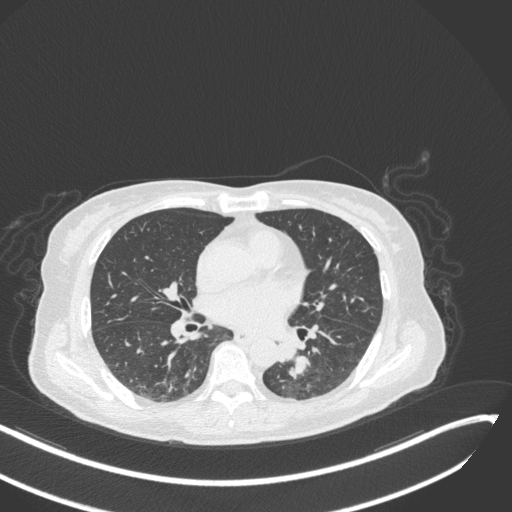
Chest CT, one axial slice; slice 129 of 342 in the series (ordered by position); 120 kVp; lung window (W 1500 / L -600 HU); 1 mm slice thickness; 512 × 512 image matrix, field of view 400 × 400 mm. Female patient, age 64 years. Case-level facts recorded for this patient, not image findings: clinical TNM (as recorded): T3 N1 M1.
Structures marked on this image (bounding box drawn by a radiologist):
- lung tumour (recorded histology: small cell carcinoma): bounding box <275,340,310,382> (left, top, right, bottom; pixels)